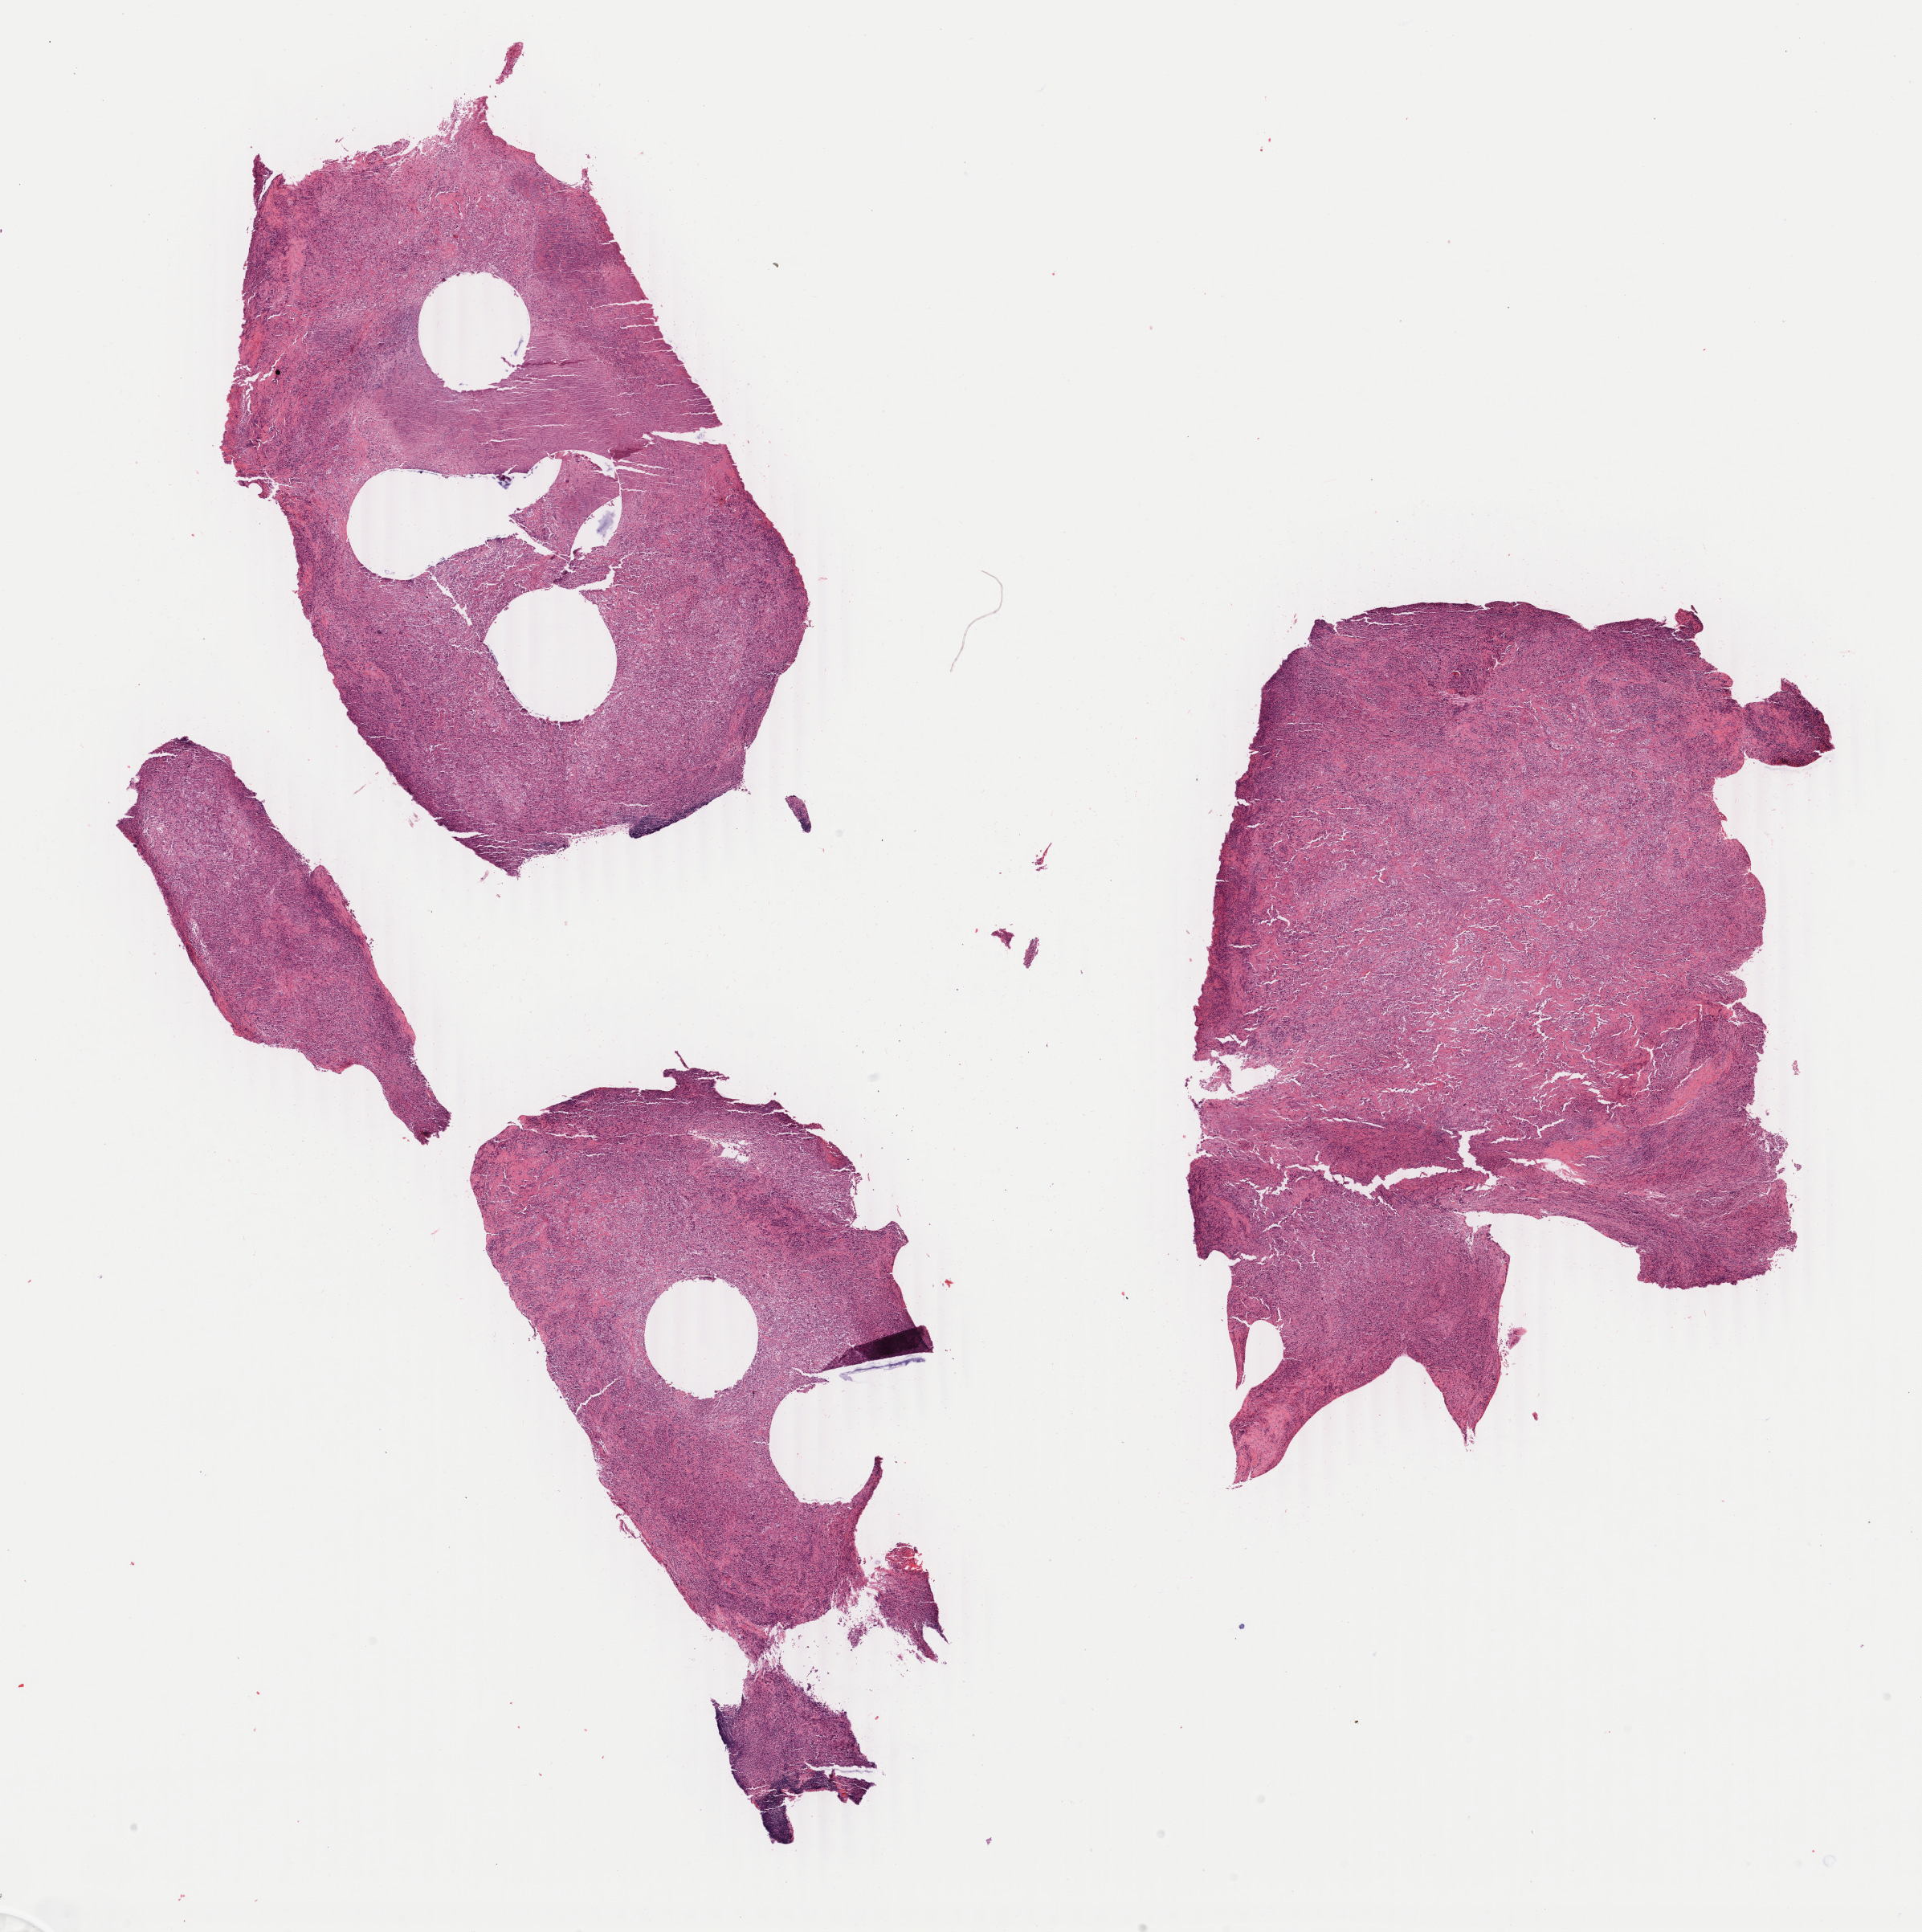
Digitized H&E-stained section, low-resolution overview of the scanned area, about 19.0 x 19.1 mm, tumor tissue, anatomic site: lung (left). Patient: male, 65 years old.
- histologic diagnosis: Carcinoma, undifferentiated, NOS